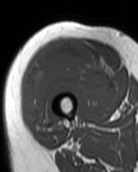
MRI of an extremity soft-tissue mass, one axial slice. MR volume resampled by the dataset authors to the PET/CT grid (not the native acquisition matrix). 3.27 mm slice thickness. 138 × 172 image matrix. Female patient. From the clinical record (not read from this slice): histological type: pleiomorphic undifferentiated sarcoma; grade: high; site of the primary tumour: right quadricep.
Outlined on this slice (expert contour drawn on MRI and transferred to this co-registered scan by the dataset authors):
- gross tumour volume including surrounding oedema: bounding box <25,43,109,129> (left, top, right, bottom; pixels)
- gross tumour volume (mass): <25,43,109,129>